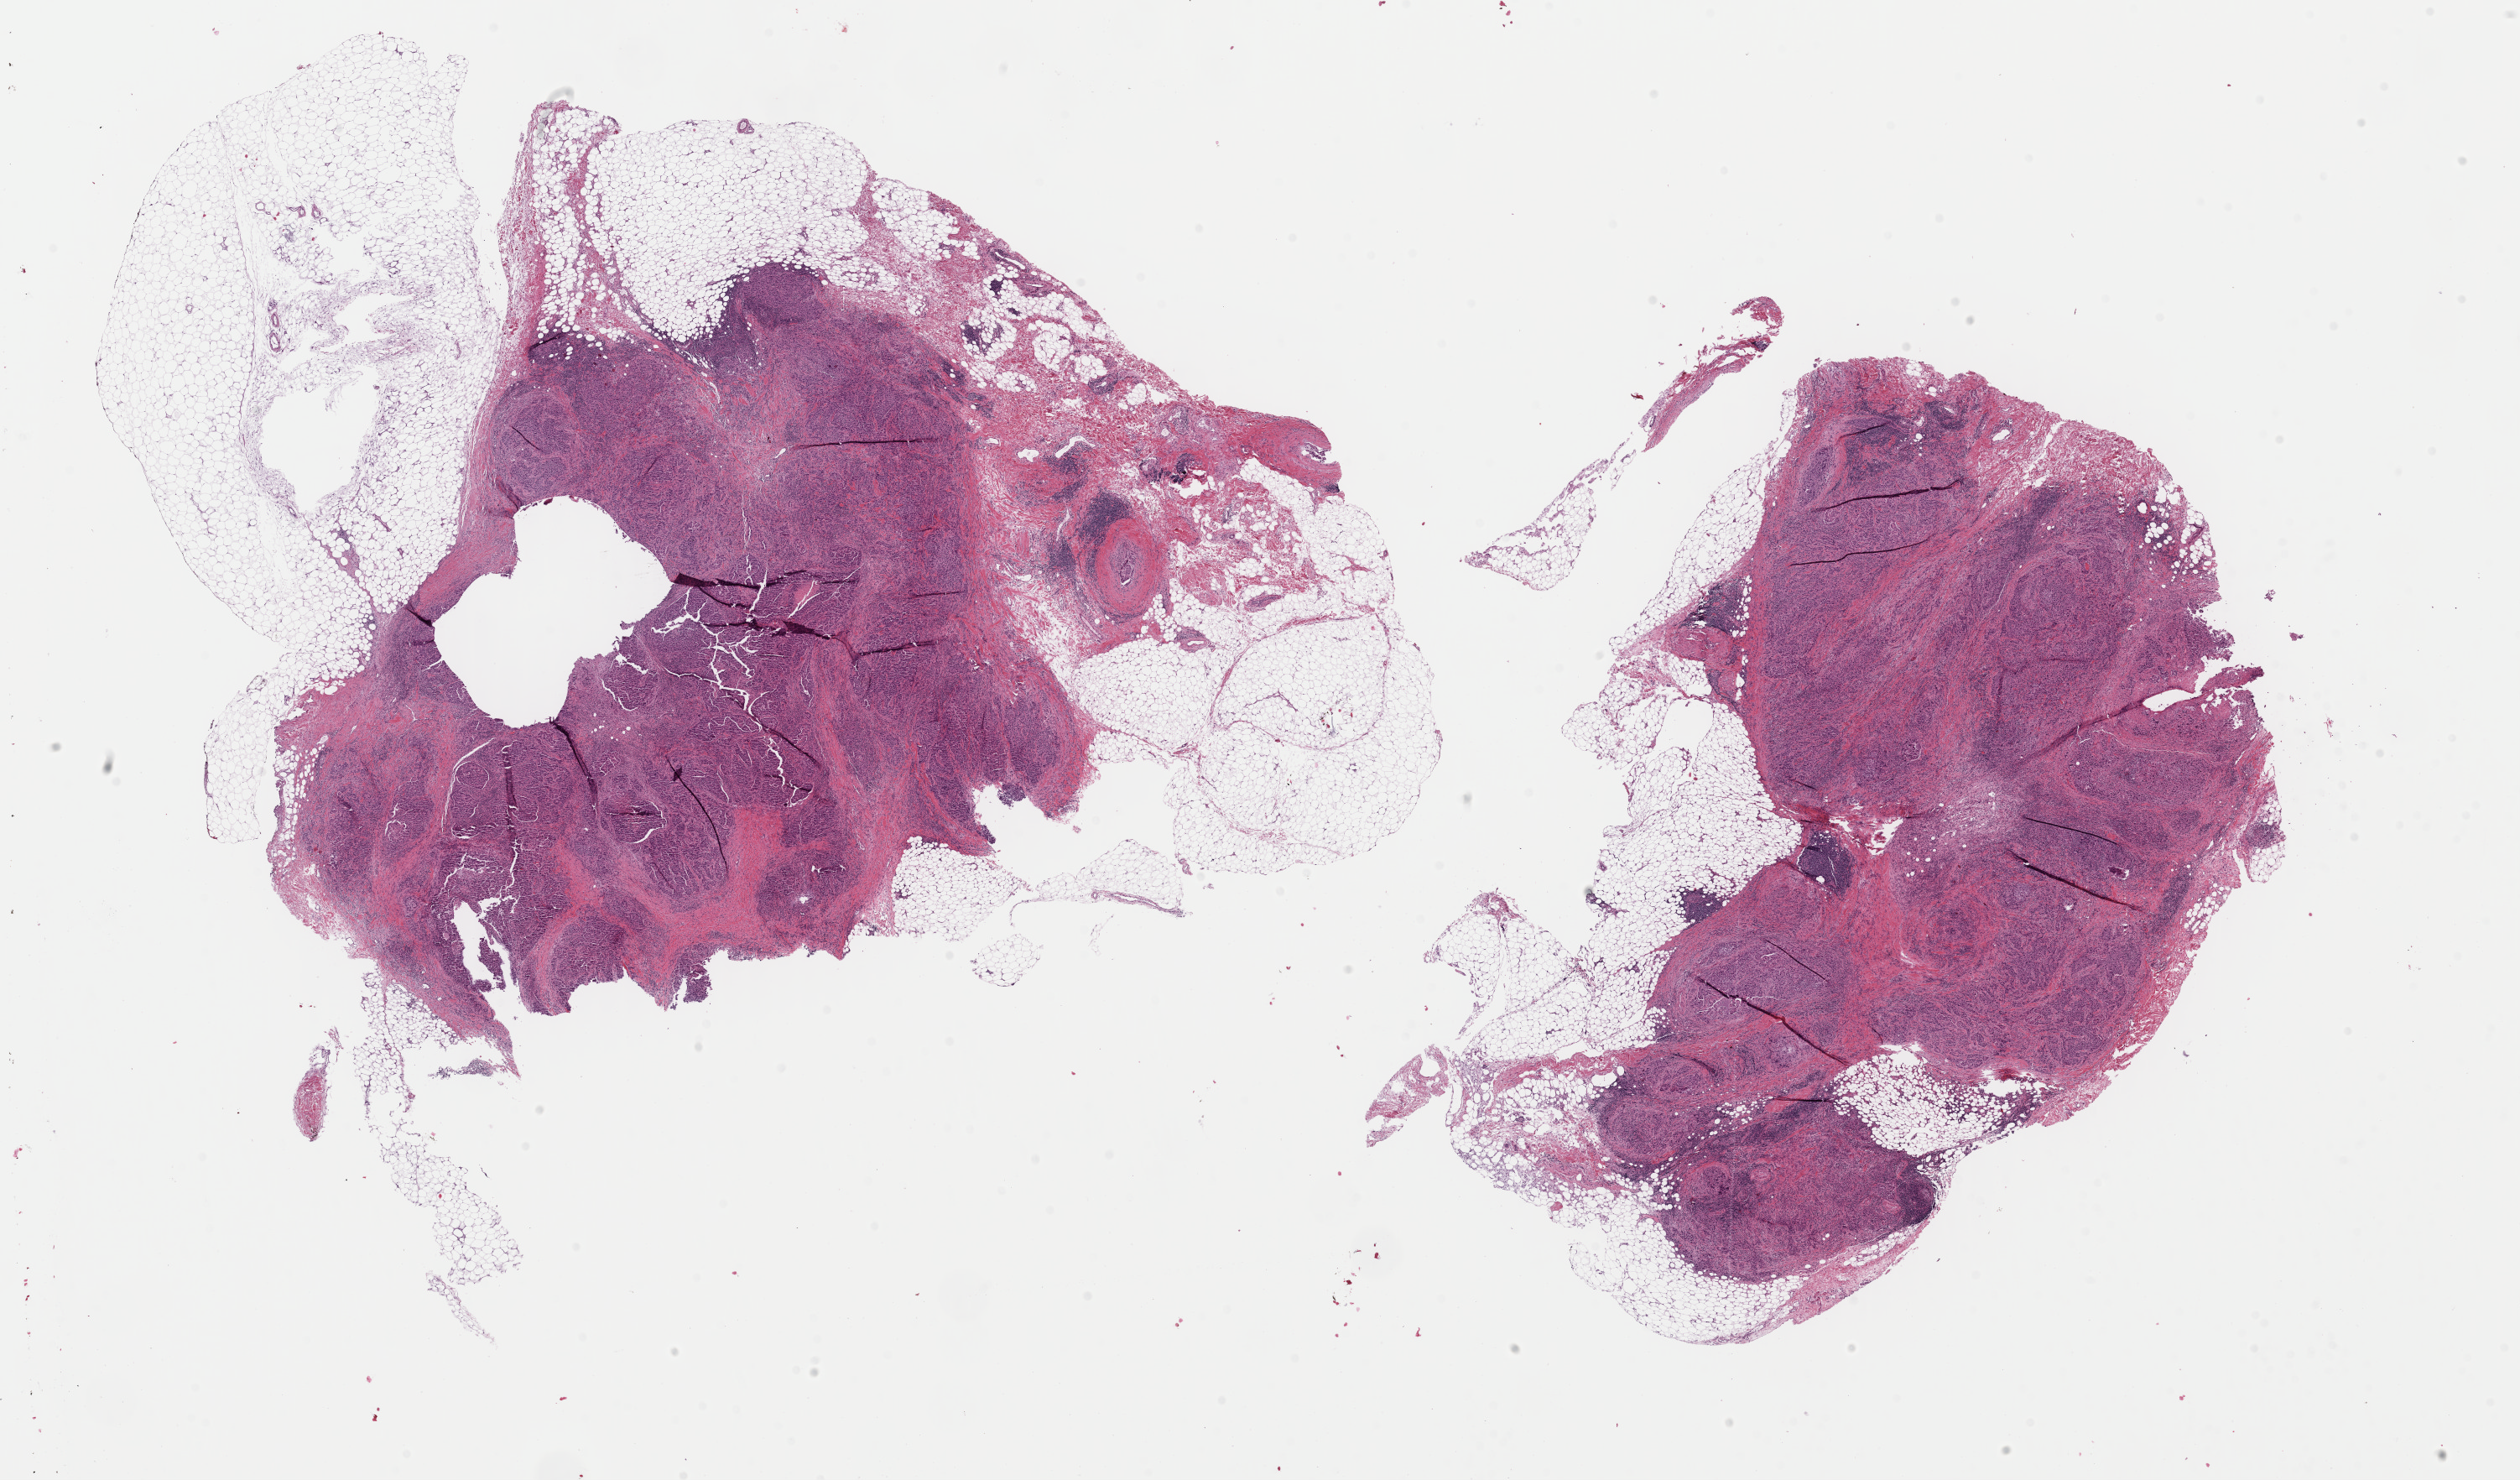
Hematoxylin and eosin (H&E) stained whole-slide image — shown as a low-resolution overview of the whole scanned area (about 23.7 x 13.9 mm); formalin-fixed paraffin-embedded (FFPE) diagnostic section; breast, primary tumour sample. Patient sex: female.
TNM: T1 N0 M0. AJCC pathologic stage: I (6th edition). Histologic diagnosis: Infiltrating duct carcinoma, NOS.